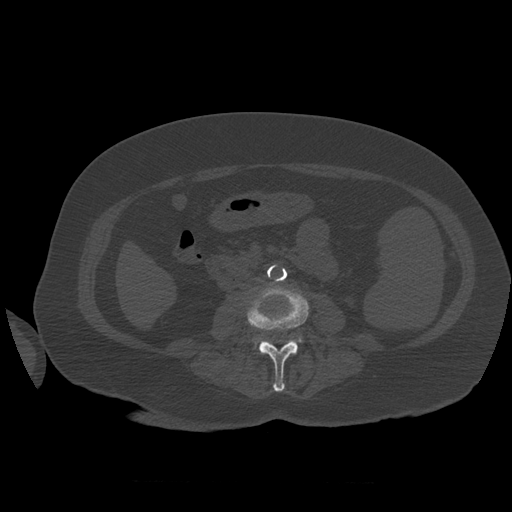
CT including the spine, one axial slice. Reconstruction kernel STANDARD. Bone window (W 1800 / L 400 HU). 1.25 mm slice thickness. 512 × 512 image matrix, field of view 404 × 404 mm. Patient age 81 years. Case-level facts recorded for this patient, not image findings: primary cancer: renal.
Structures marked on this image (semi-automatic segmentation, software-assisted and operator-edited):
- L3 vertebra: bounding box <247,283,309,392> (left, top, right, bottom; pixels)
- L4 vertebra: <295,338,302,343>